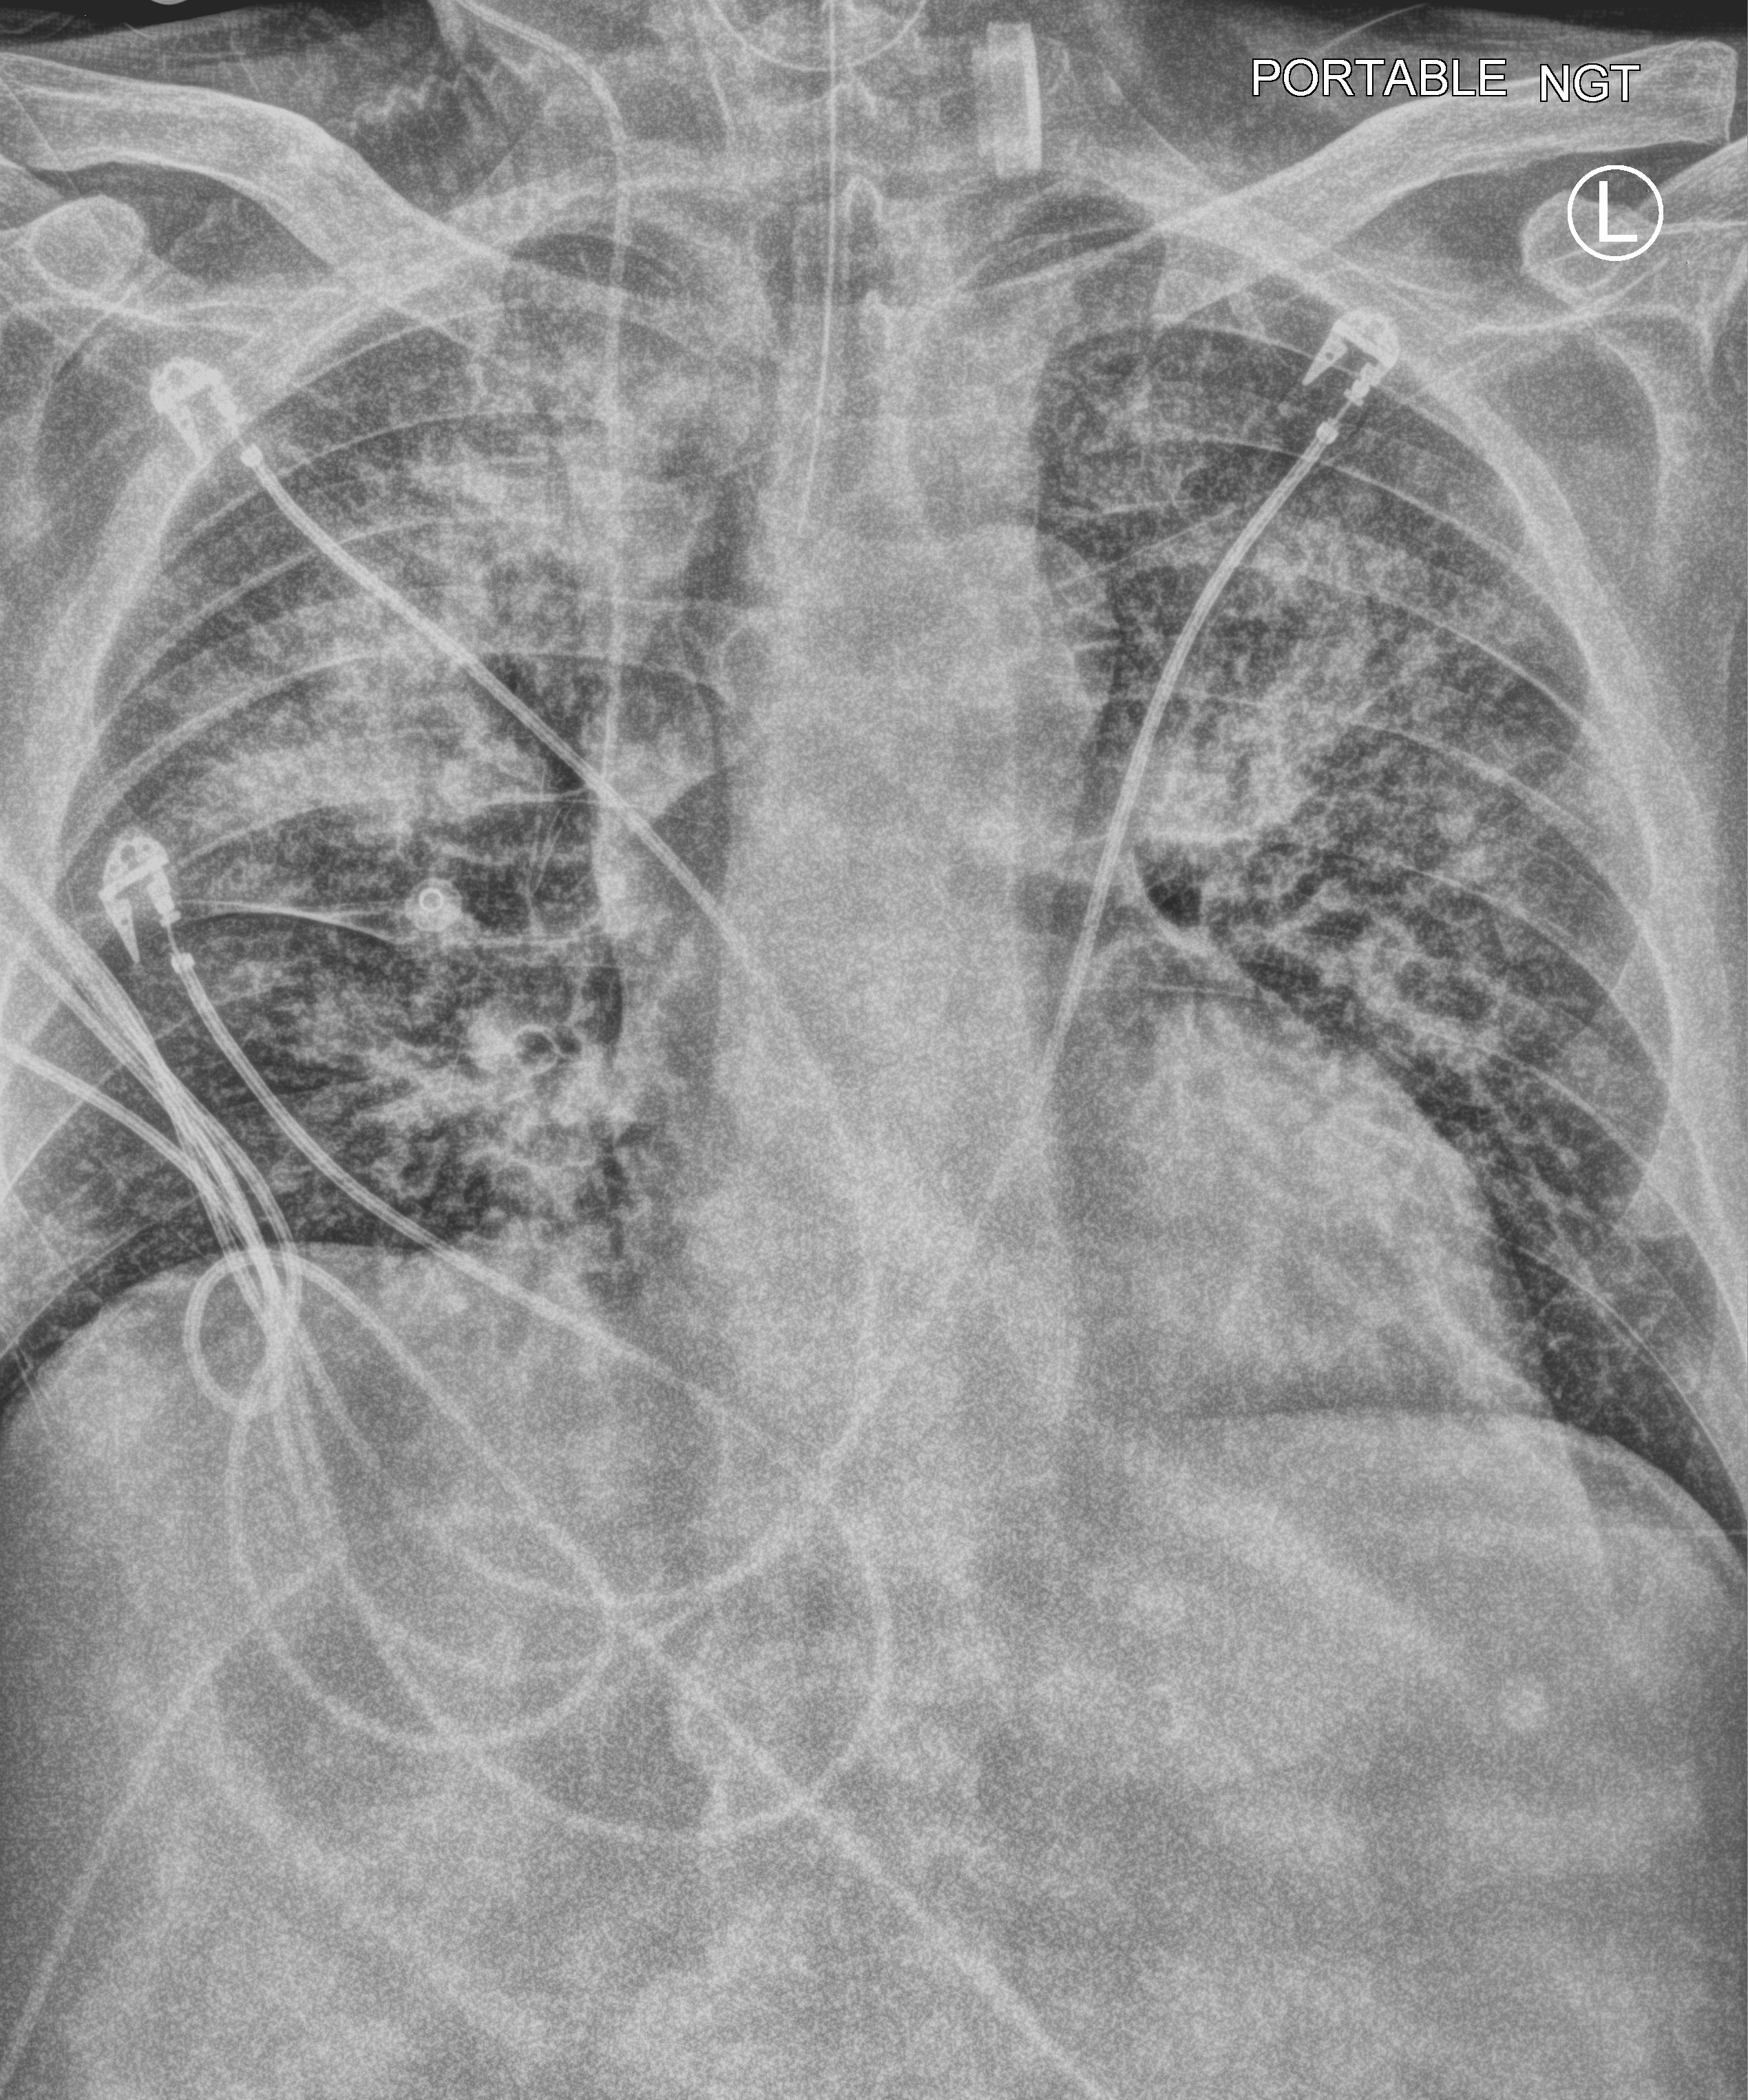
Bedside chest radiograph (computed radiography). Male patient hospitalised with COVID-19, age 75–90 years.
Hospital-stay facts (about this admission, not read from this image; timing relative to this image not recorded): smoking status (admission record): never; mechanically ventilated during this hospital stay: yes; admitted to intensive care during this hospital stay: yes.